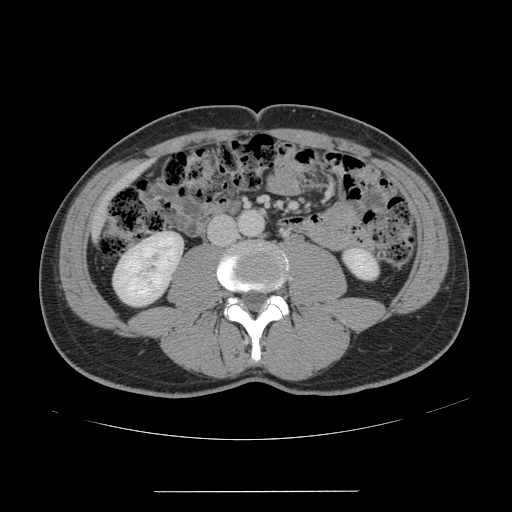
Contrast-enhanced abdominal CT, one axial slice. Position 27 of 178 along the scan axis. 120 kVp. Intravenous contrast given. Soft-tissue window (W 400 / L 40 HU). 2.5 mm slice thickness. 512 × 512 image matrix, field of view 401 × 401 mm. Male patient, age 53 years. Case-level facts recorded for this patient, not image findings: diagnosis: colorectal cancer liver metastases, imaged before liver resection; multiple liver metastases: yes; largest metastasis: 2.4 cm; chemotherapy before resection: yes.
Structures marked on this image (expert manual segmentation):
- liver: bounding box (x1, y1, x2, y2) in pixels: (99, 166, 146, 225)